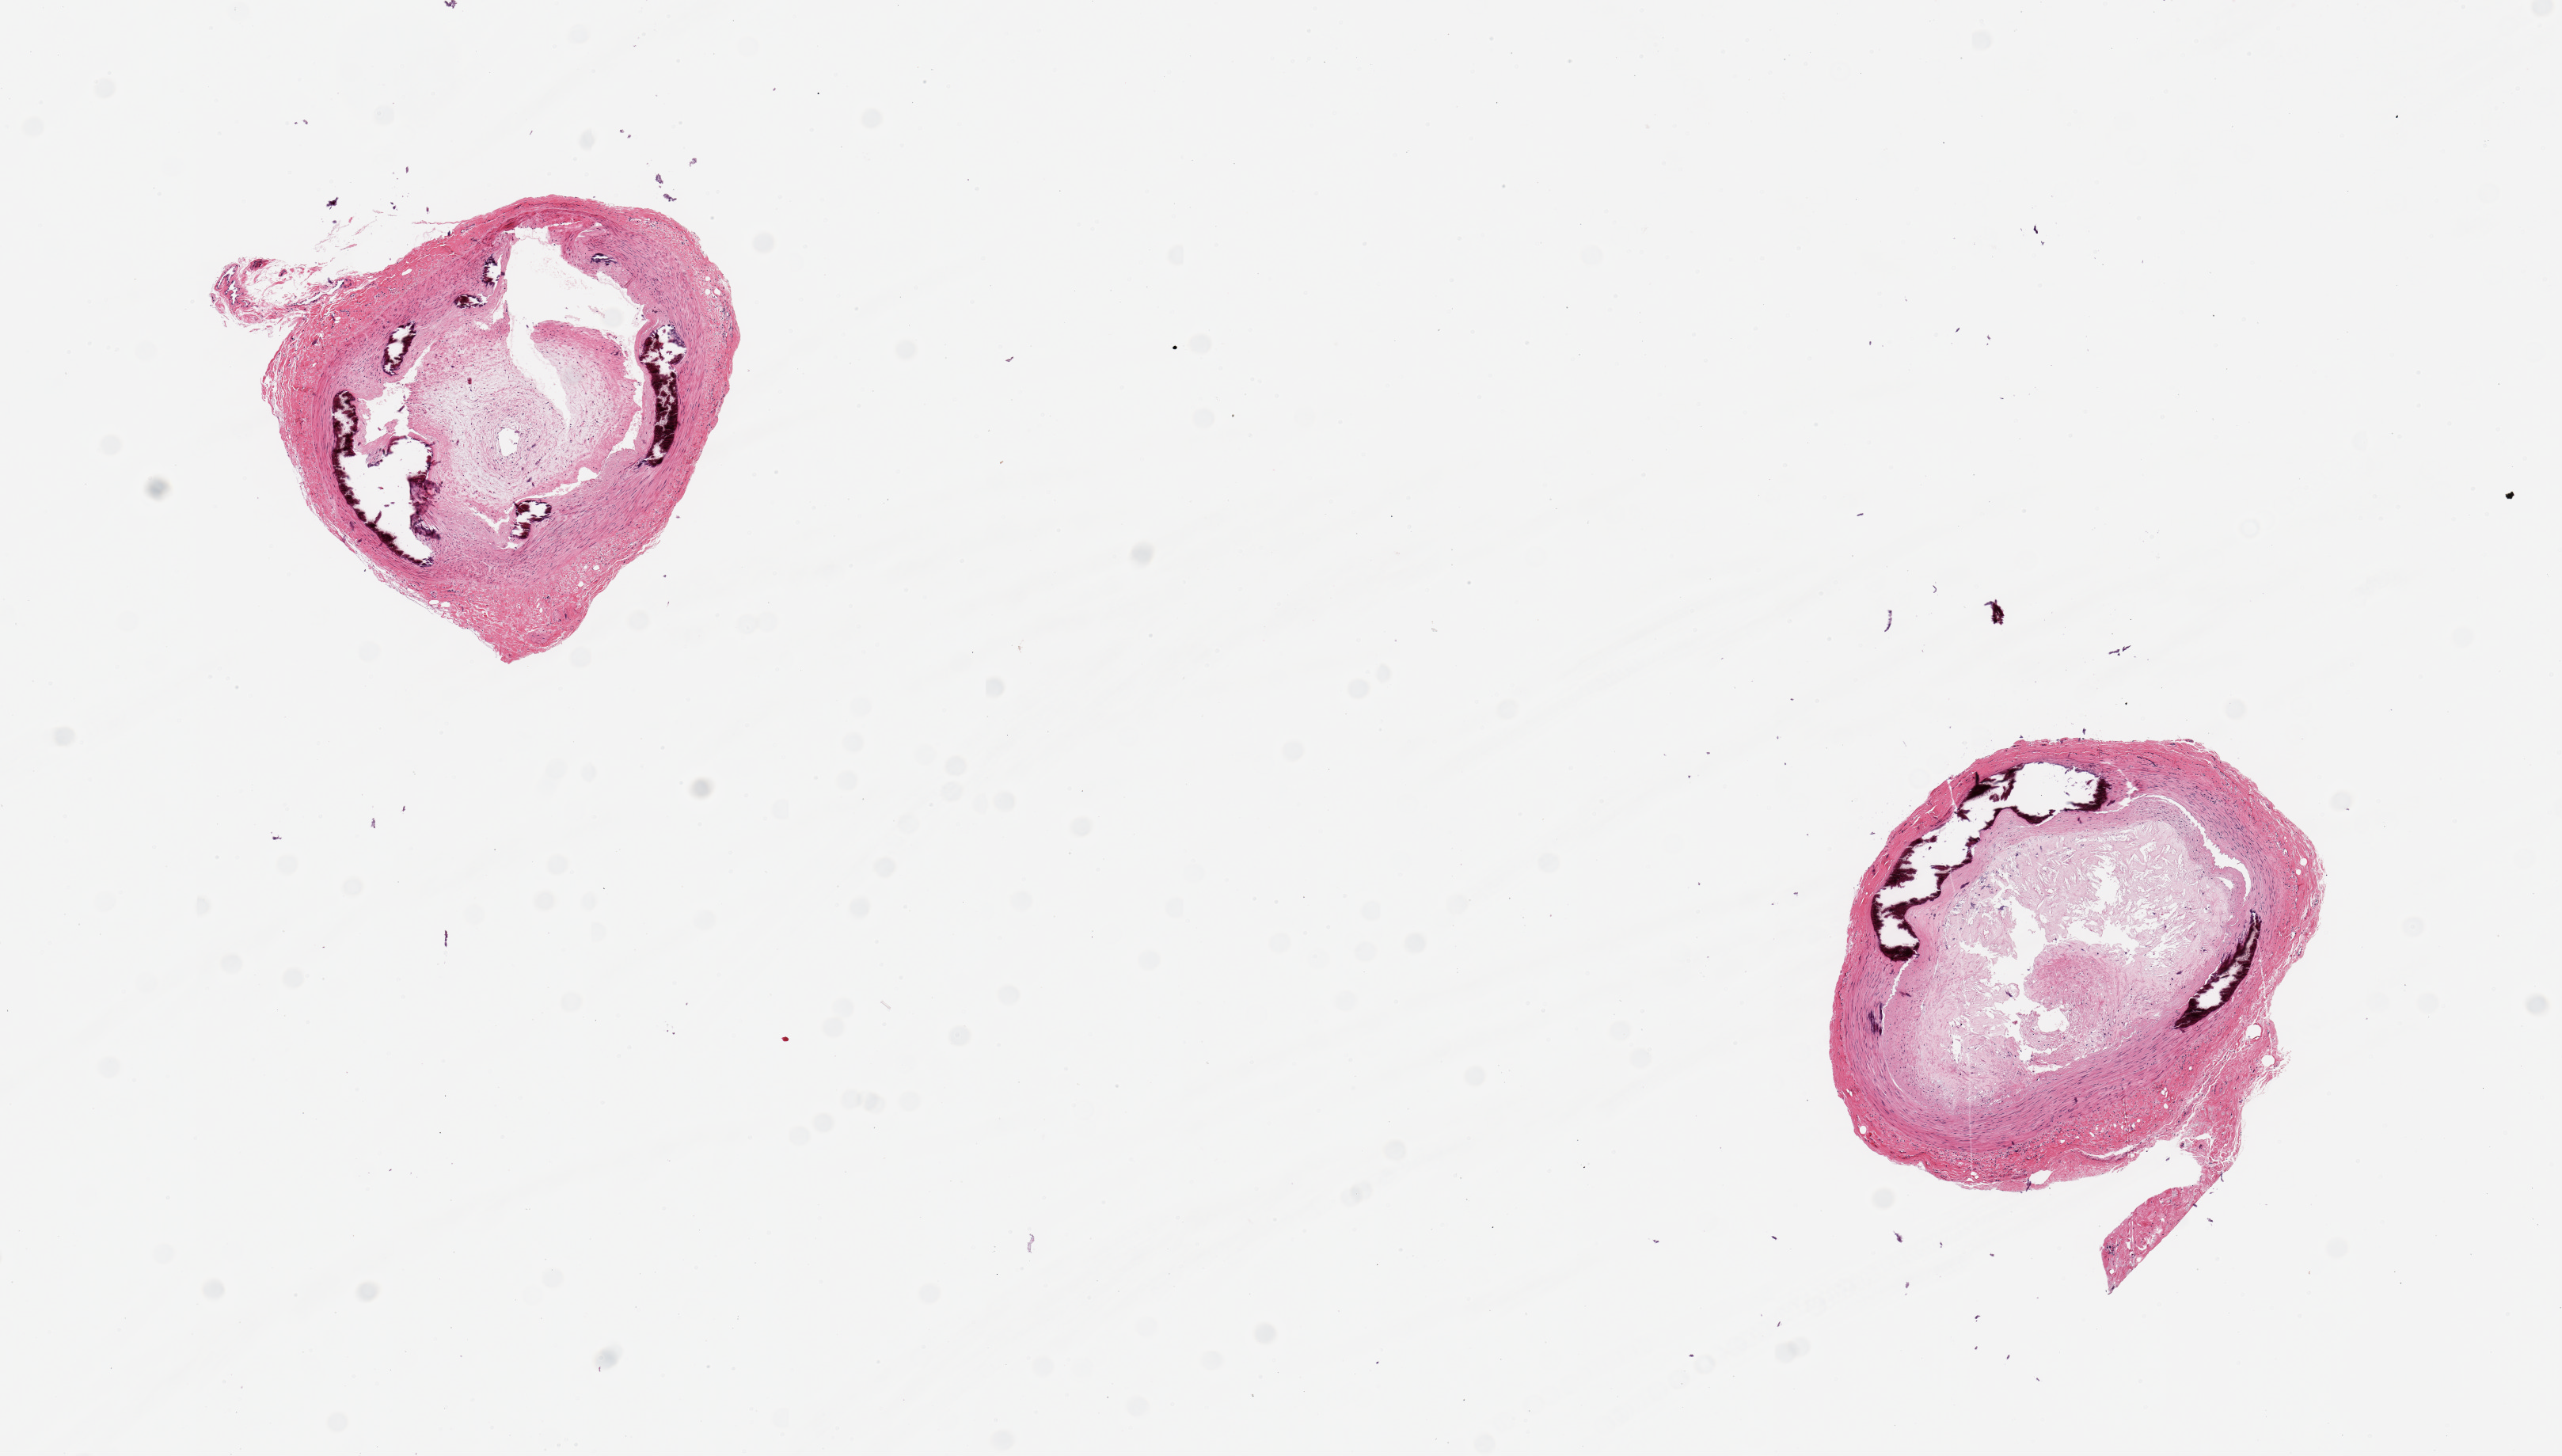
Digitized hematoxylin and eosin (H&E)-stained section, a low-resolution overview of the entire scanned area, about 12.8 x 7.3 mm (slide scanned at 20x), PAXgene-fixed, paraffin-embedded tissue, target tissue: tibial artery, tissue donor sample. Female donor.
• pathologist's review note for this sample: 2 pieces, 2.5x2.5 & 3x2mm; severe occlusive atherosclerosis; medial calcification